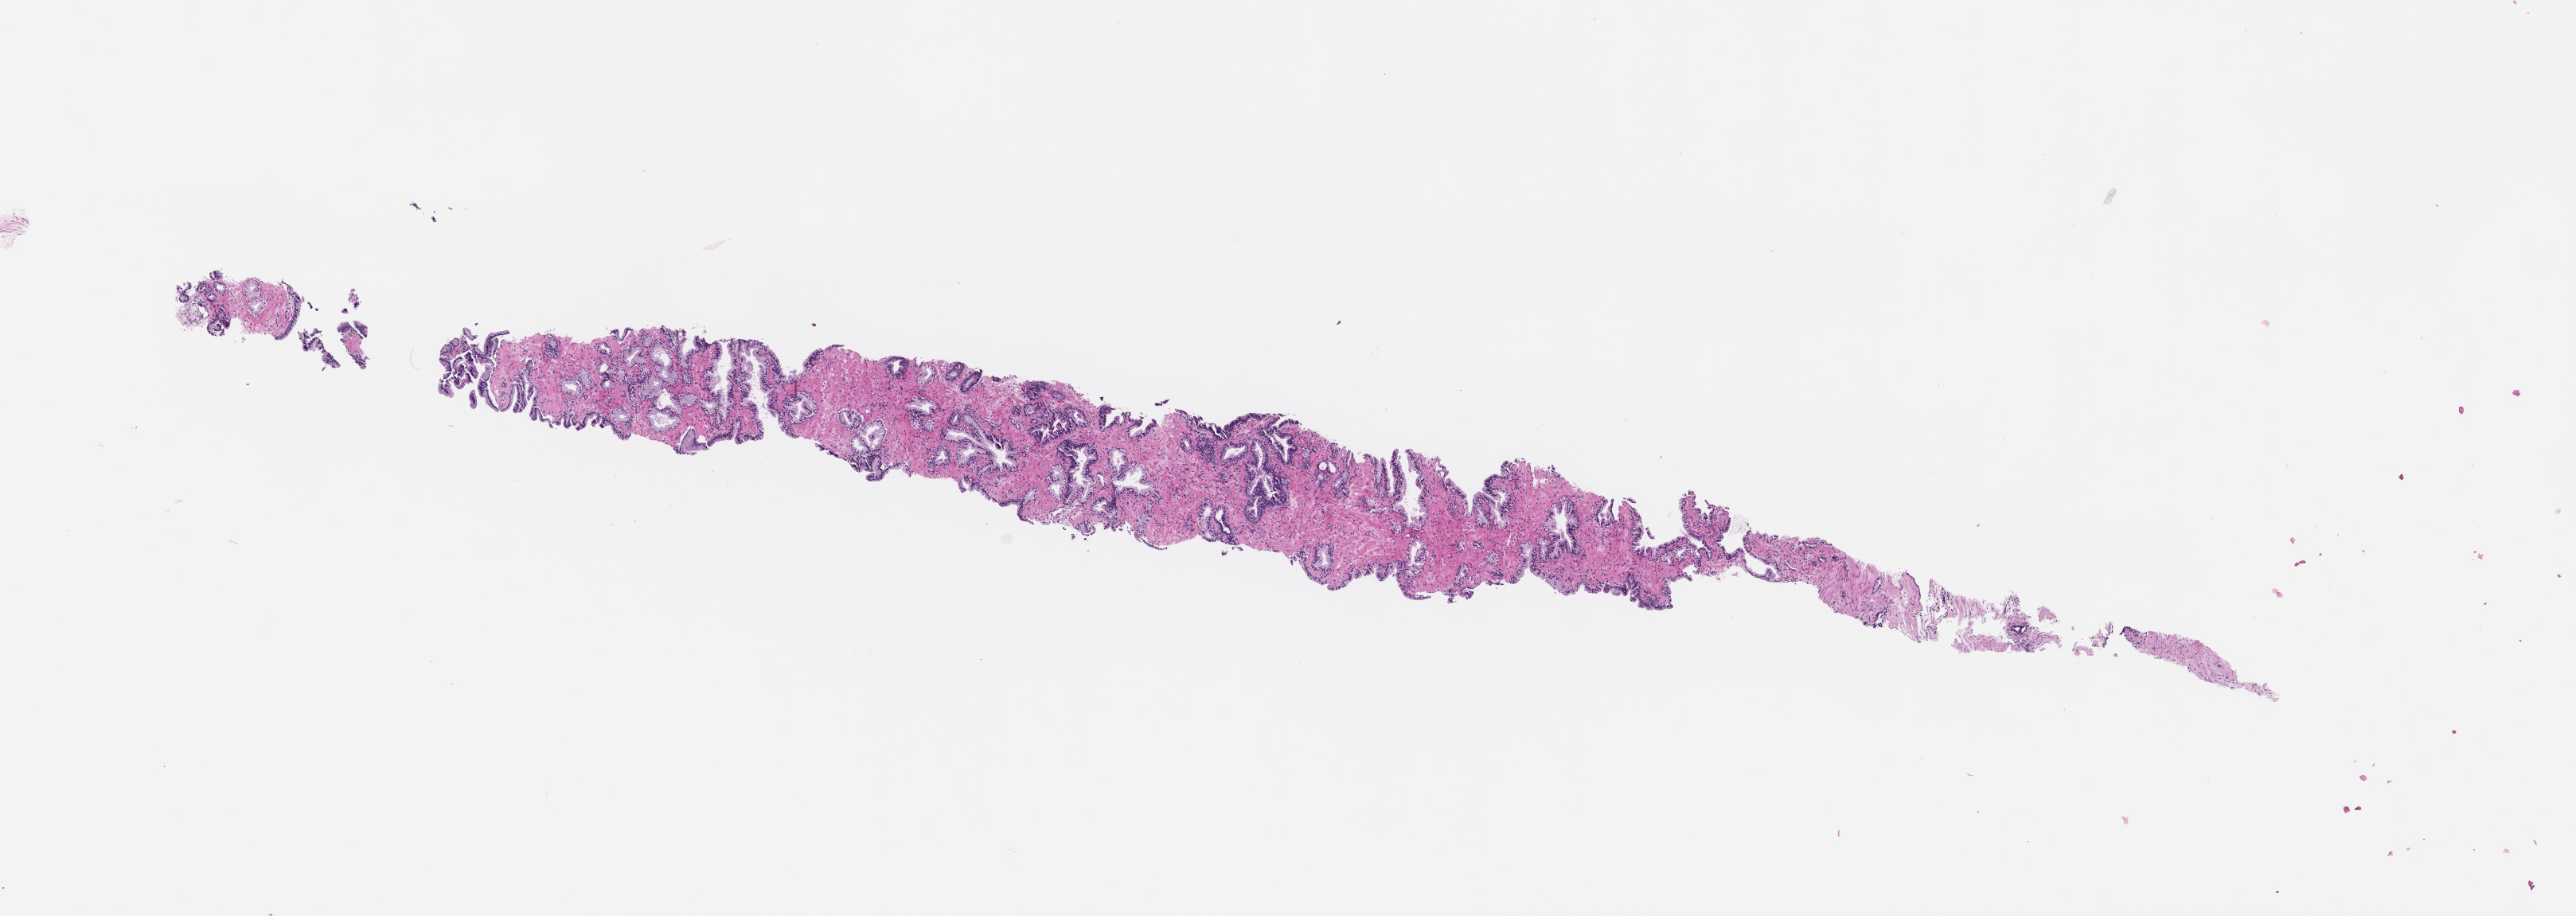
Hematoxylin and eosin (H&E) whole-slide image — shown as a low-resolution overview of the whole scanned area (about 13.1 x 4.6 mm). Formalin-fixed, paraffin-embedded (FFPE) tissue. Tissue site: prostate. Archival tissue. Patient sex: male.
- this section: primary tumor
- diagnosis: Prostate Carcinoma